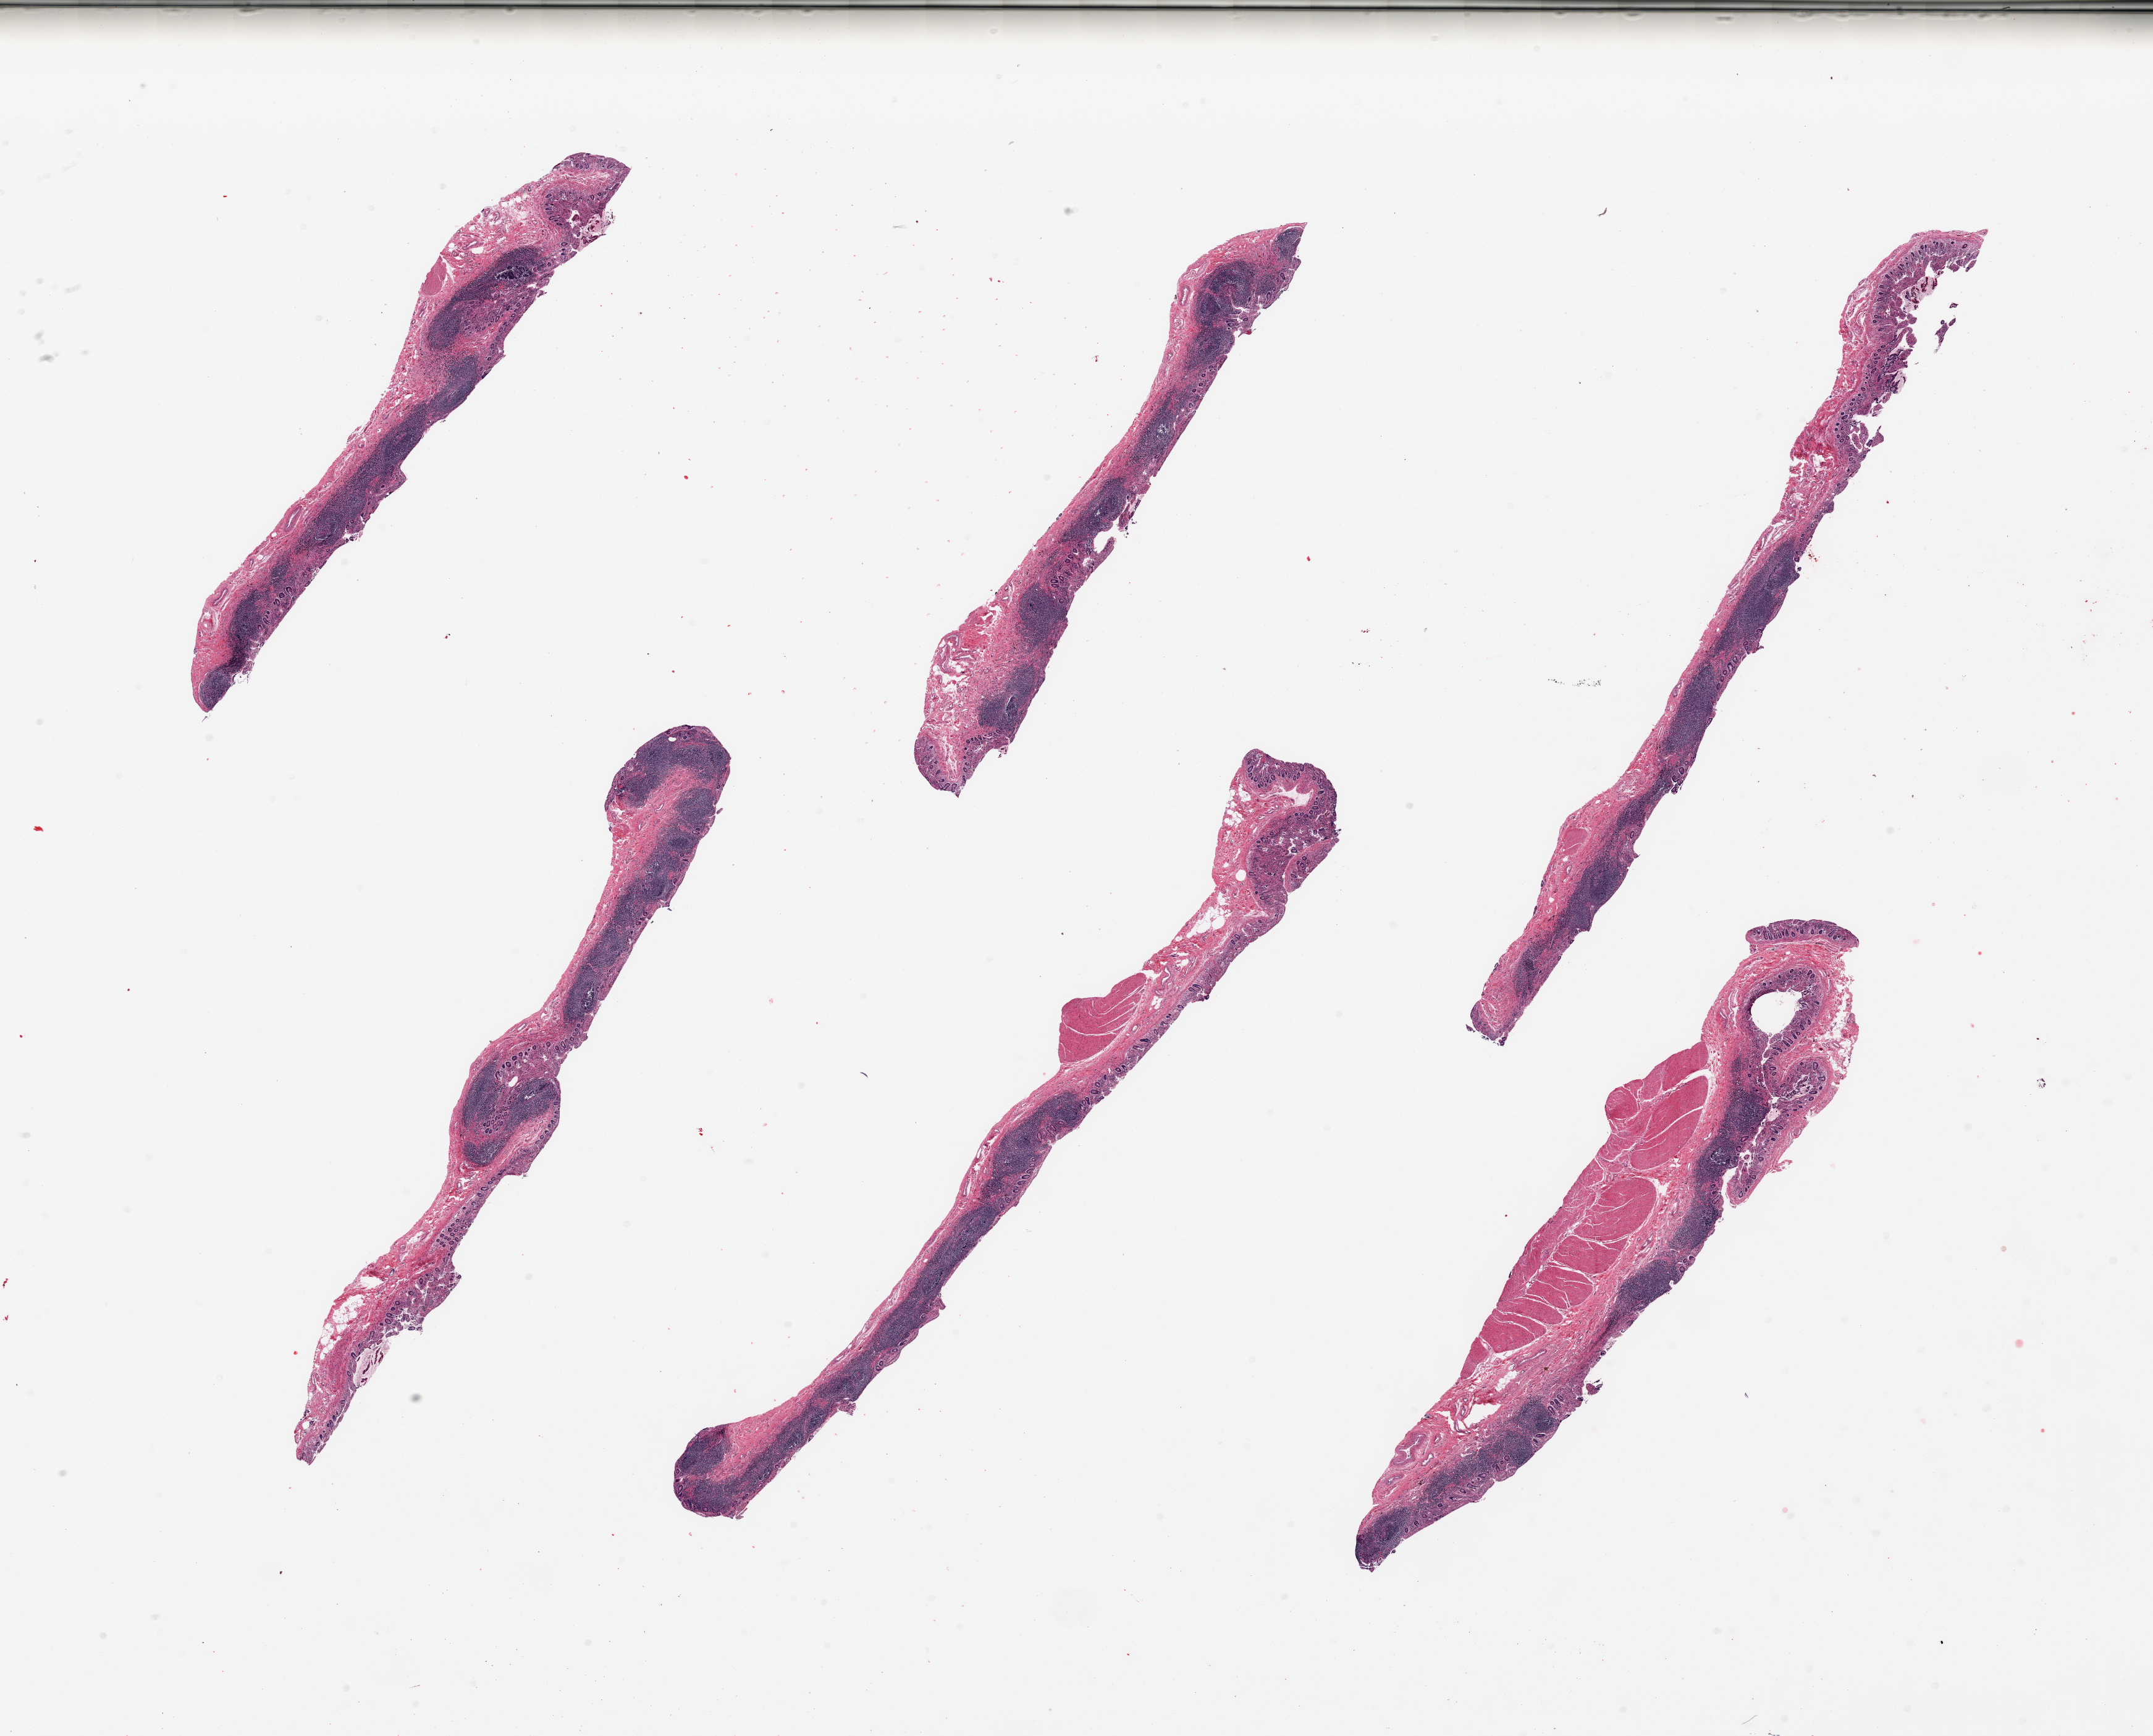
Digitized H&E-stained section — shown as a low-resolution overview of the whole scanned area (about 27.6 x 22.2 mm), PAXgene-fixed, paraffin-embedded tissue, sampled site (target tissue): ileum, donor tissue sample.
- pathologist's review note for this sample: 6 pieces, ~40% target lymphoid aggregates